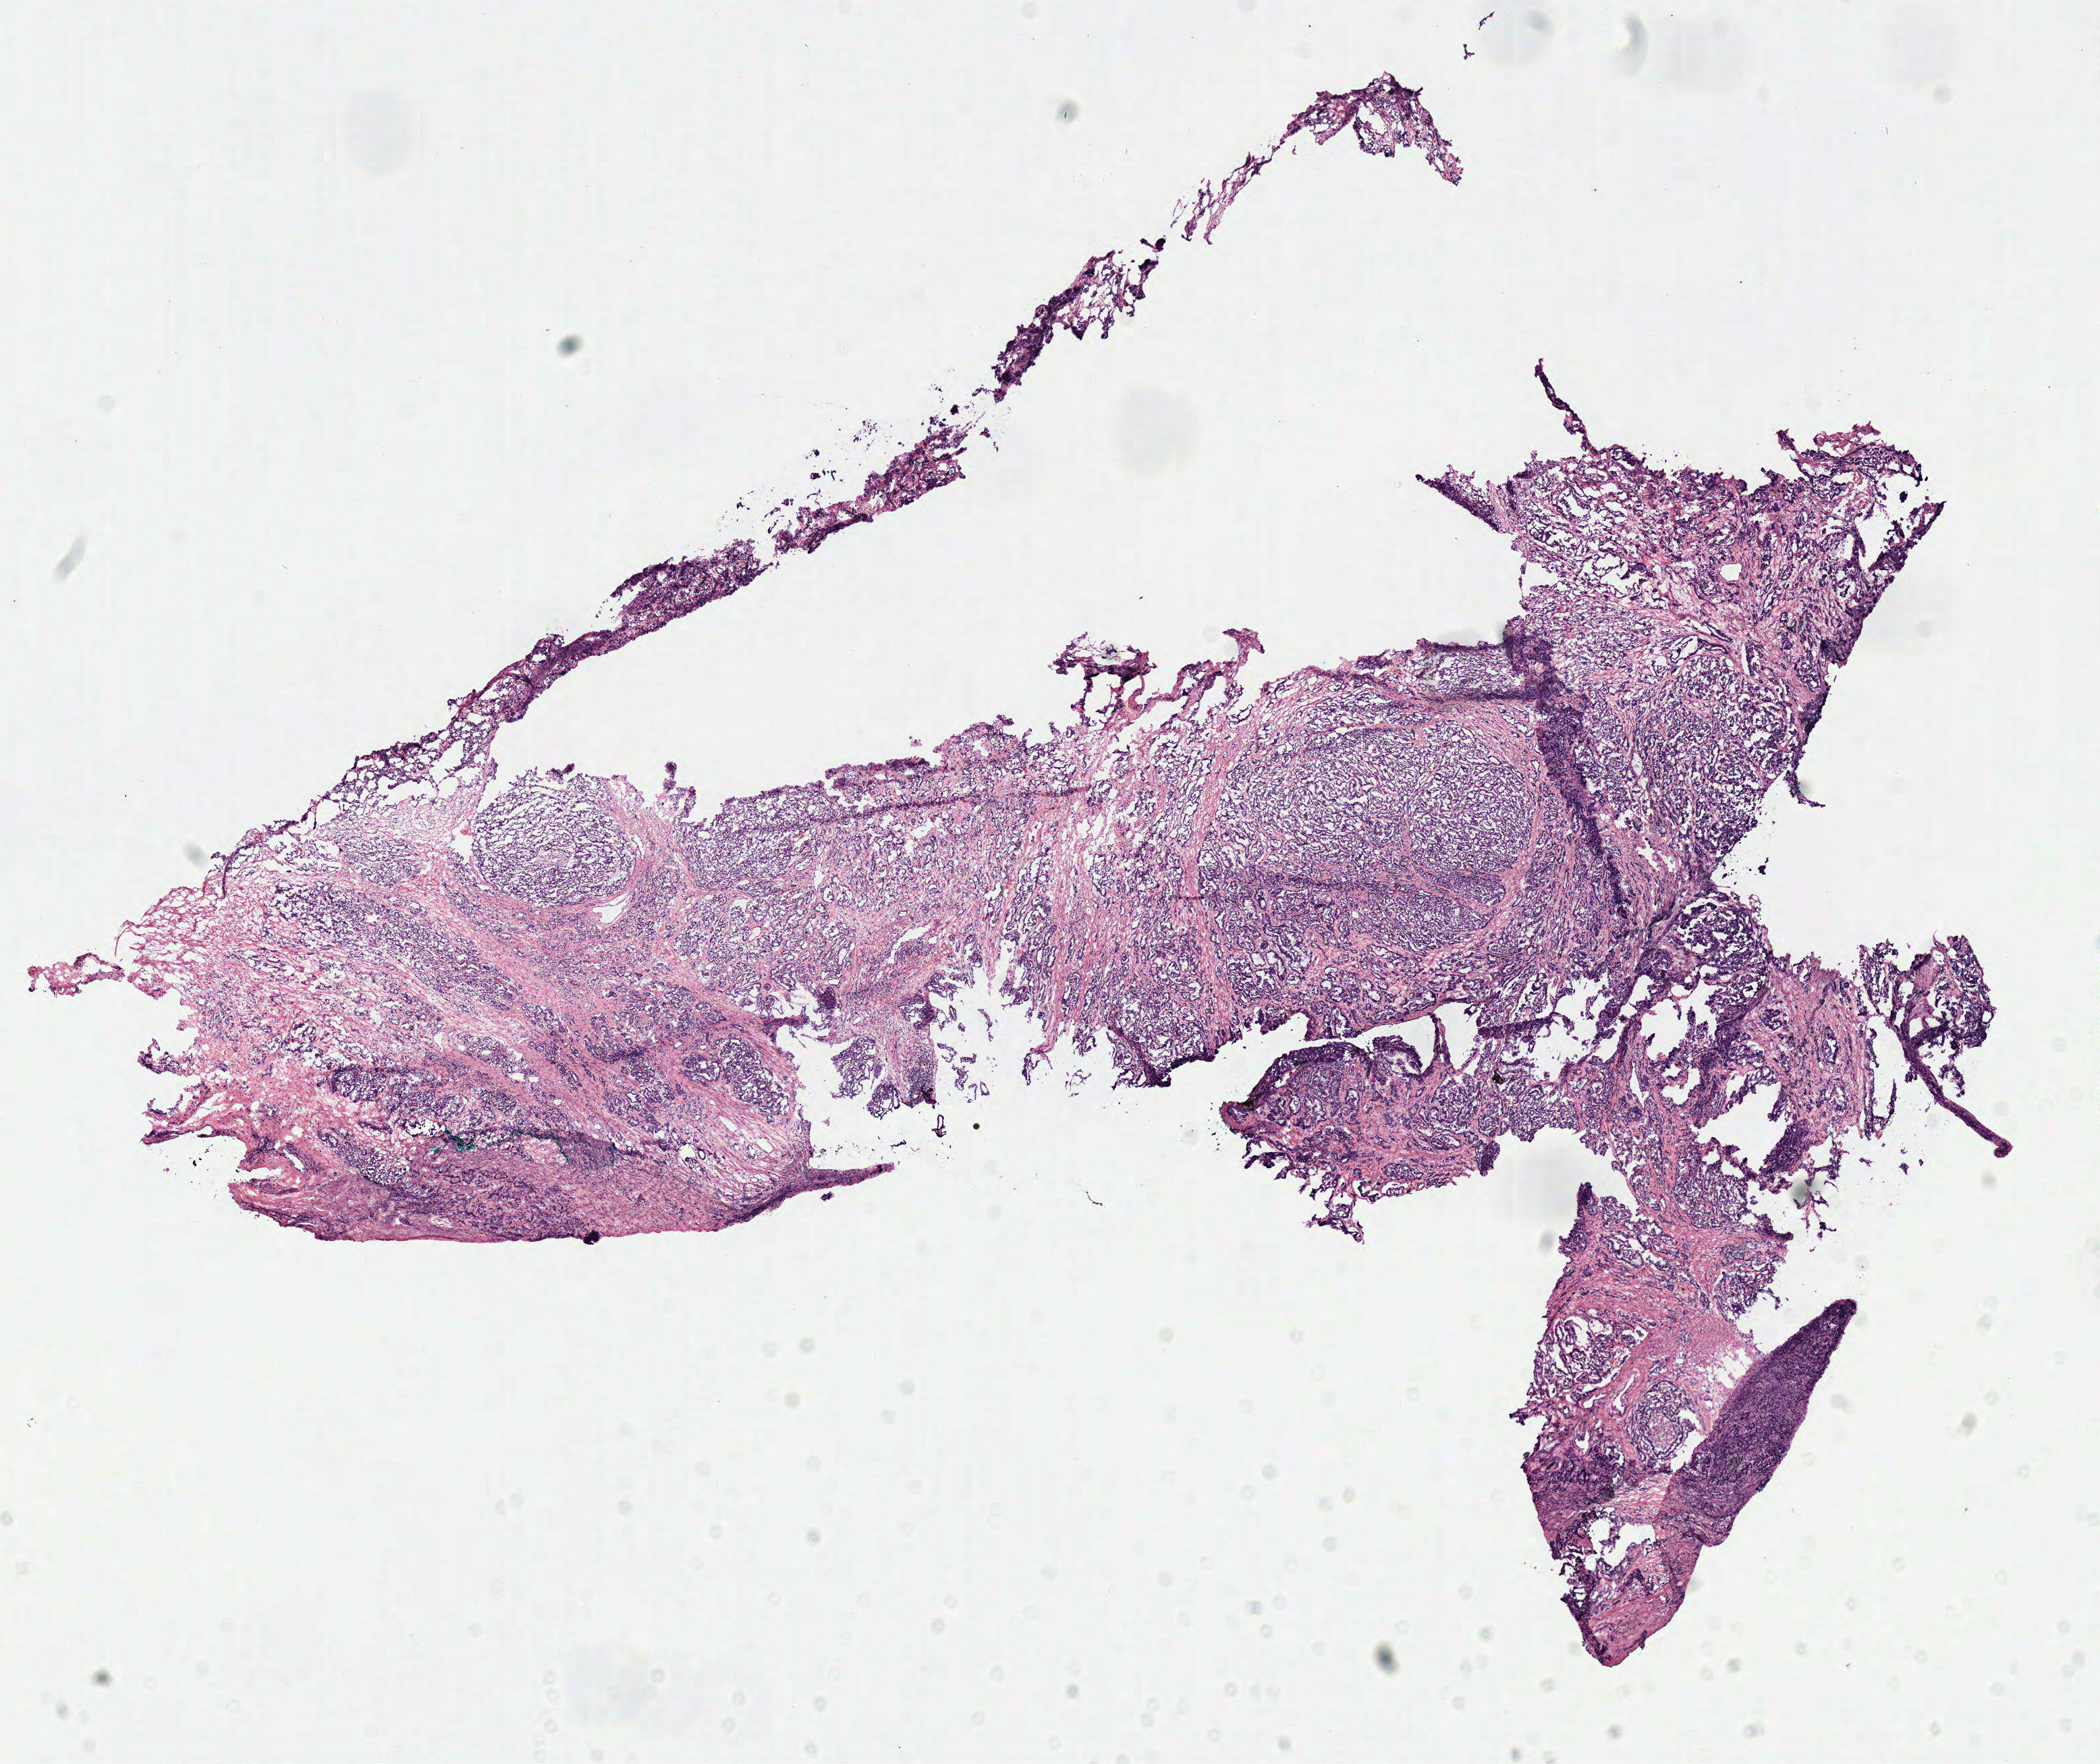
Whole-slide histology image, H&E-stained — shown as a low-resolution overview of the whole scanned area (about 12.2 x 10.3 mm, slide scanned at 40x), frozen section from the top of the tissue portion, primary tumour sample from the prostate. Male, age 57 years at initial diagnosis. Gleason score: 7 (4+3). Composition of this section per pathologist review: tumour cells 80%, tumour nuclei 80%, normal cells 5%, stromal cells 15%, necrosis 0%. Infiltration values recorded for this section: lymphocyte infiltration 5%, monocyte infiltration 0%, neutrophil infiltration 0%.
- laterality: bilateral
- pathologic diagnosis: Acinar cell carcinoma (prostate gland)